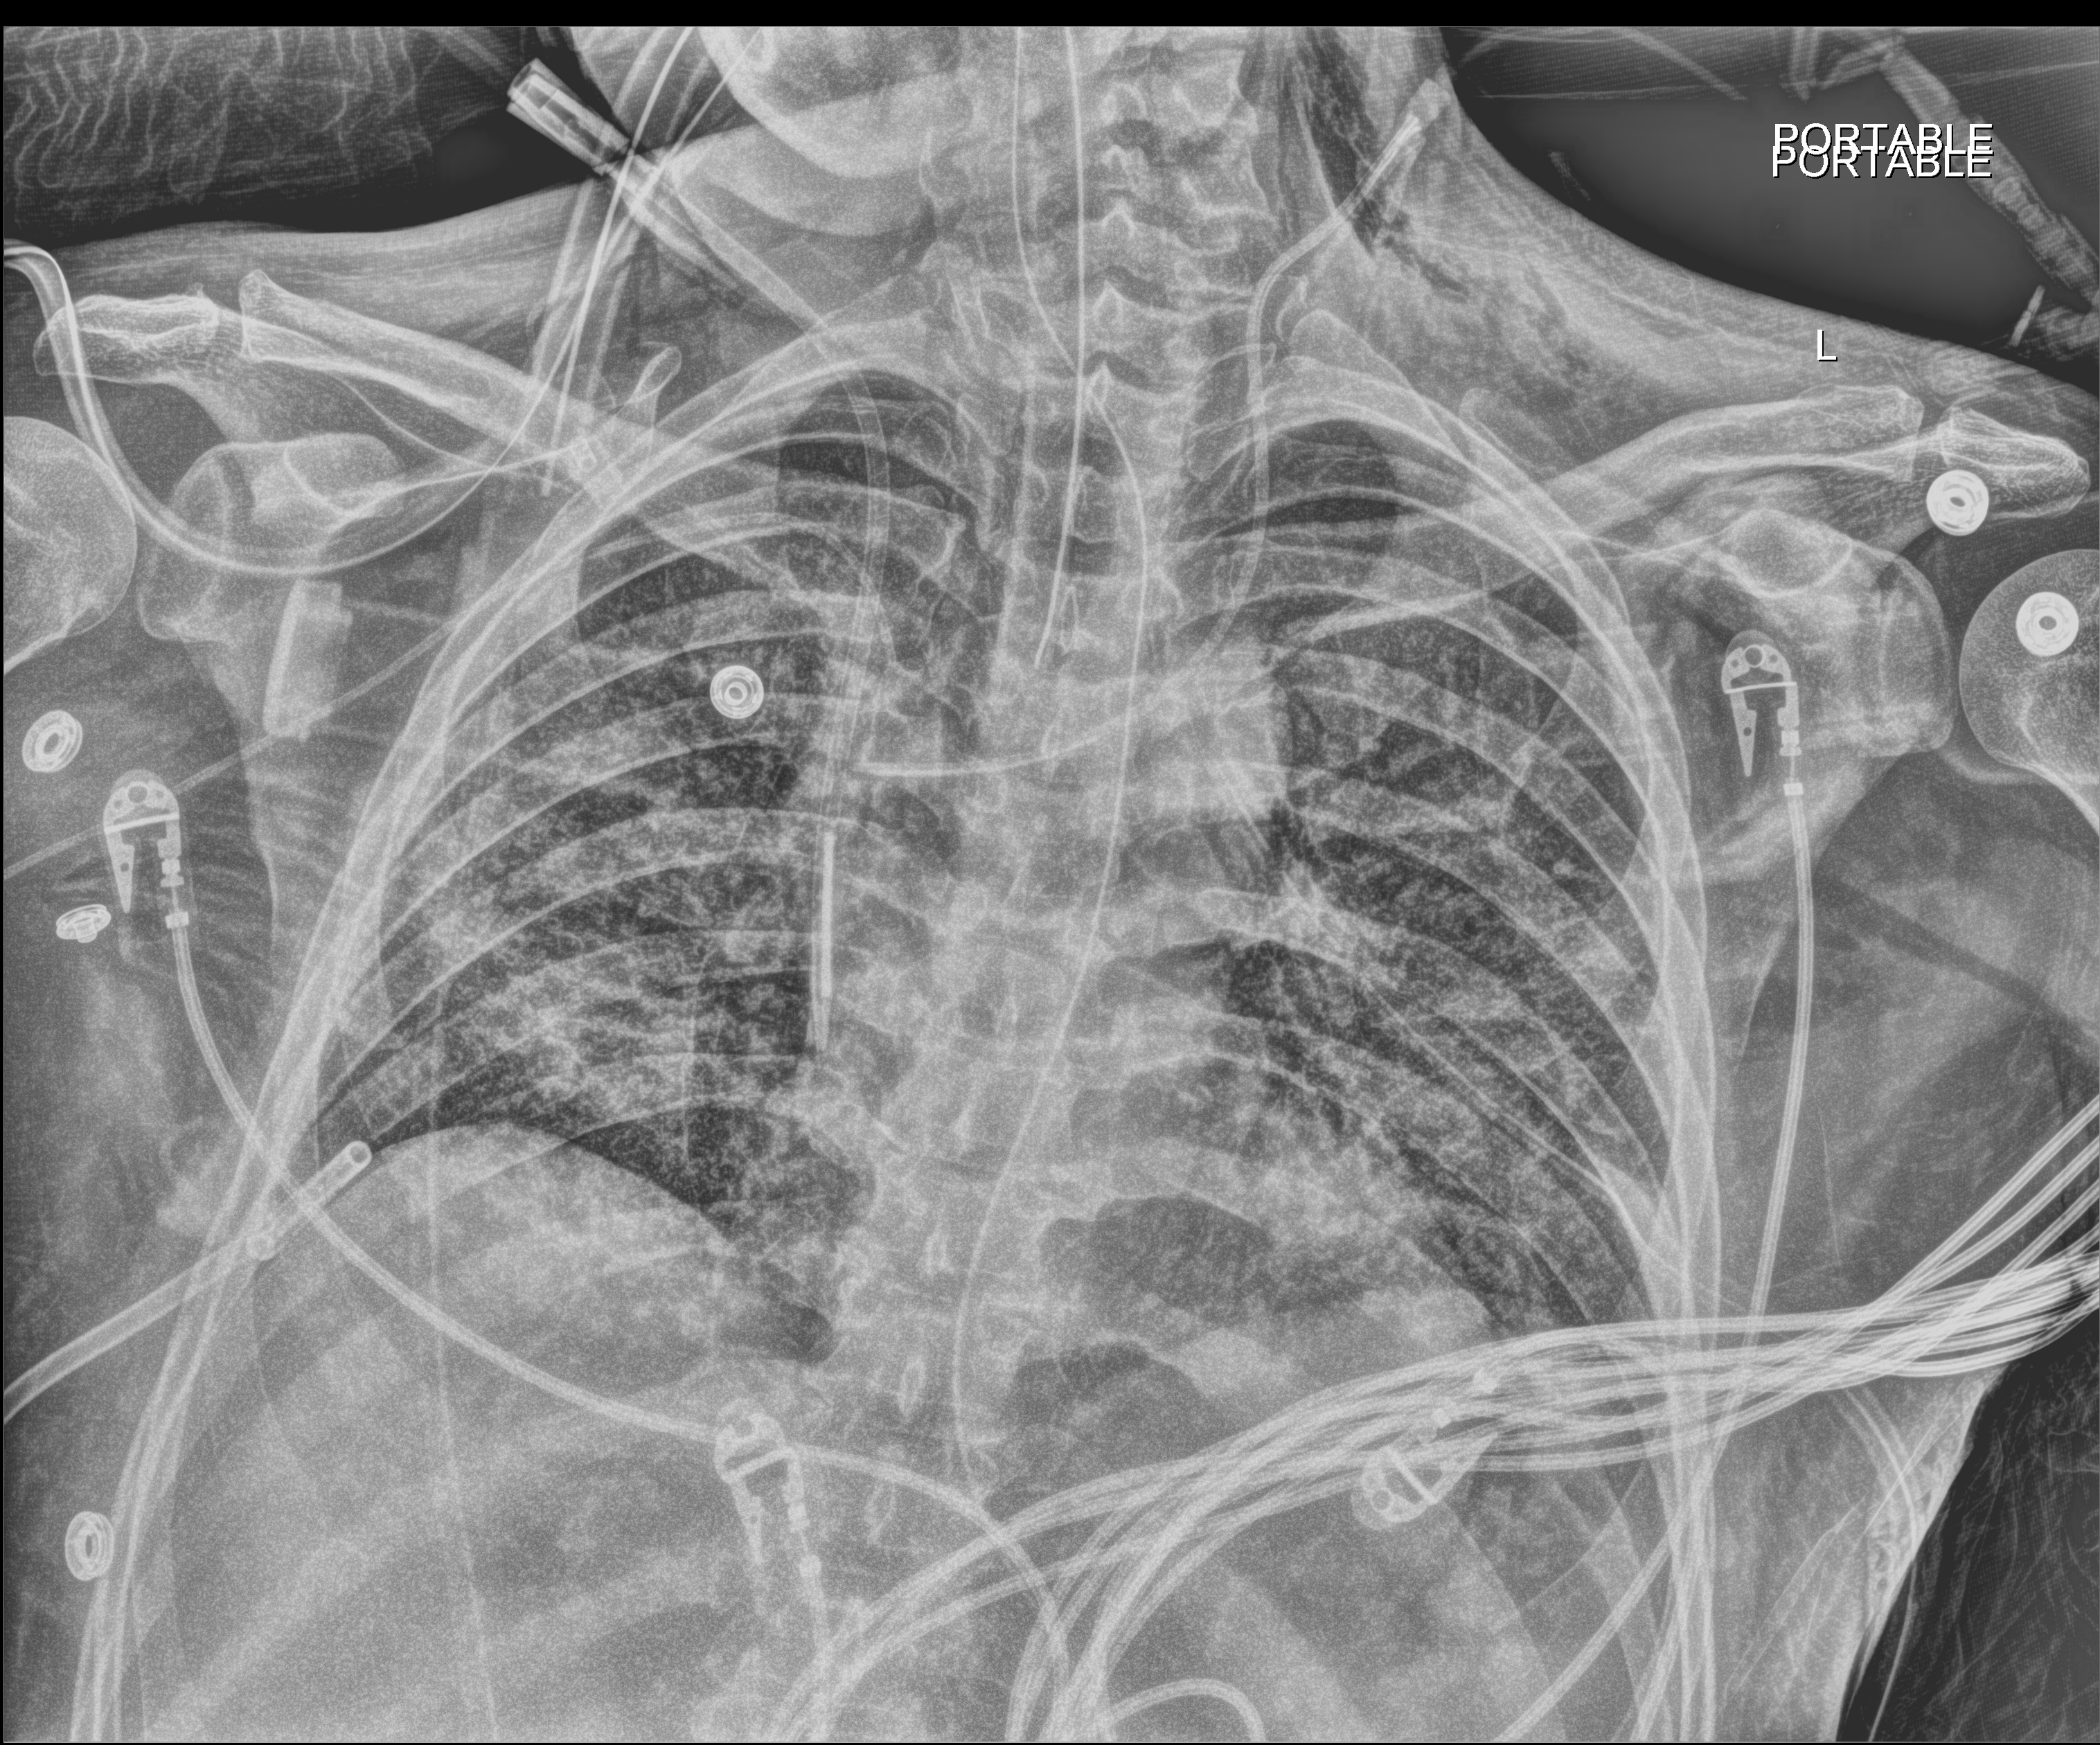
Bedside chest radiograph (digital radiography), anteroposterior (AP) projection. Male patient hospitalised with COVID-19, age 18–59 years.
From the hospital-stay record, not from the radiograph (when in the stay this image was taken is not recorded): admitted to intensive care during this hospital stay: yes; mechanically ventilated during this hospital stay: yes; other chronic lung disease (admission record): no.